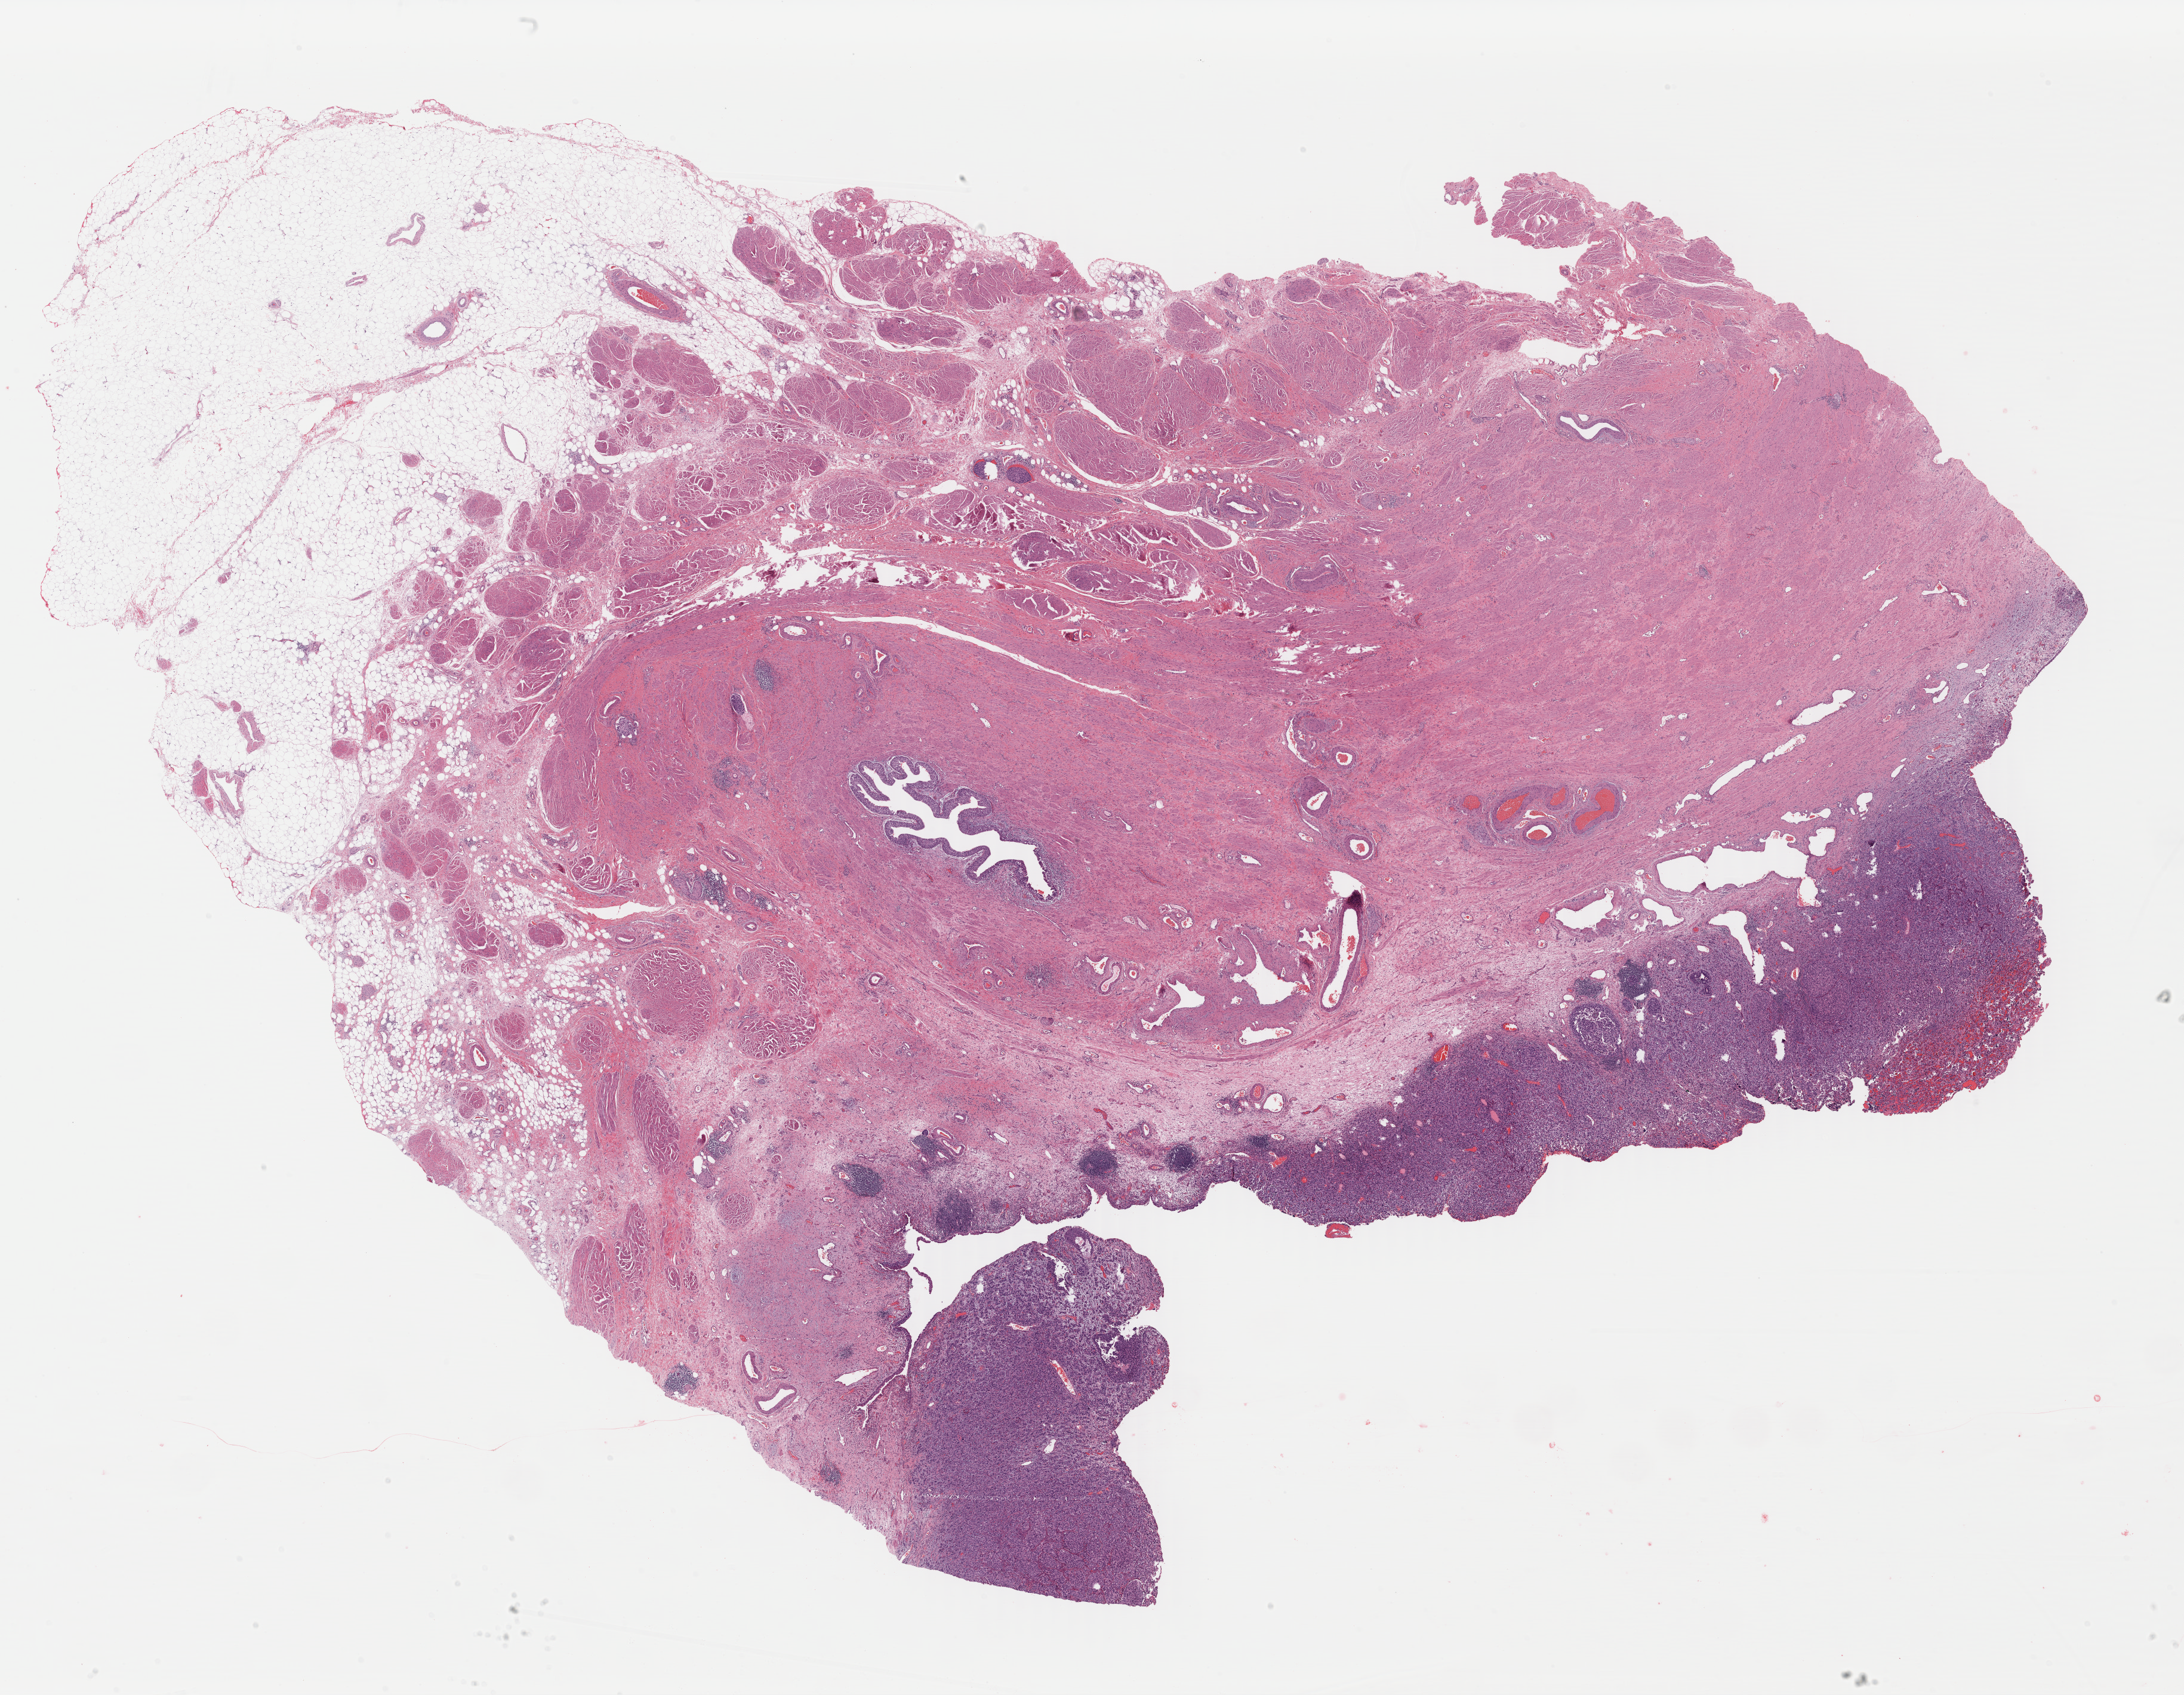
H&E whole-slide image — shown as a low-resolution overview of the whole scanned area (about 28.8 x 22.3 mm, from a 40x scan); formalin-fixed paraffin-embedded (FFPE) diagnostic section; primary tumour sample from the bladder. Patient: male, age at initial diagnosis 76 years. Histologic grade: high grade.
Lymph nodes positive (case pathology): 2 of 47 examined. AJCC pathologic stage: IV (7th edition). Diagnosis: Transitional cell carcinoma.